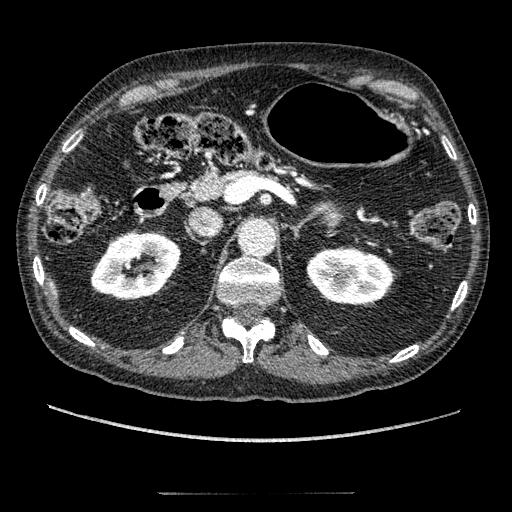
Contrast-enhanced abdominal CT, one axial slice; slice 126 of 274 in the series (ordered by position); reconstruction kernel STANDARD; 120 kVp; soft-tissue window (W 400 / L 40 HU); 512 × 512 image matrix. Patient: male, 69 years. Case-level facts recorded for this patient, not image findings: diagnosis: adrenocortical carcinoma; tumour side: left adrenal; tumour size at pathology: 6.1 cm; Ki-67 index: 10 %.
Outlined on this slice (semi-automatic segmentation, software-assisted and operator-edited):
- mass: bounding box [x1, y1, x2, y2] px = [324, 206, 340, 227]